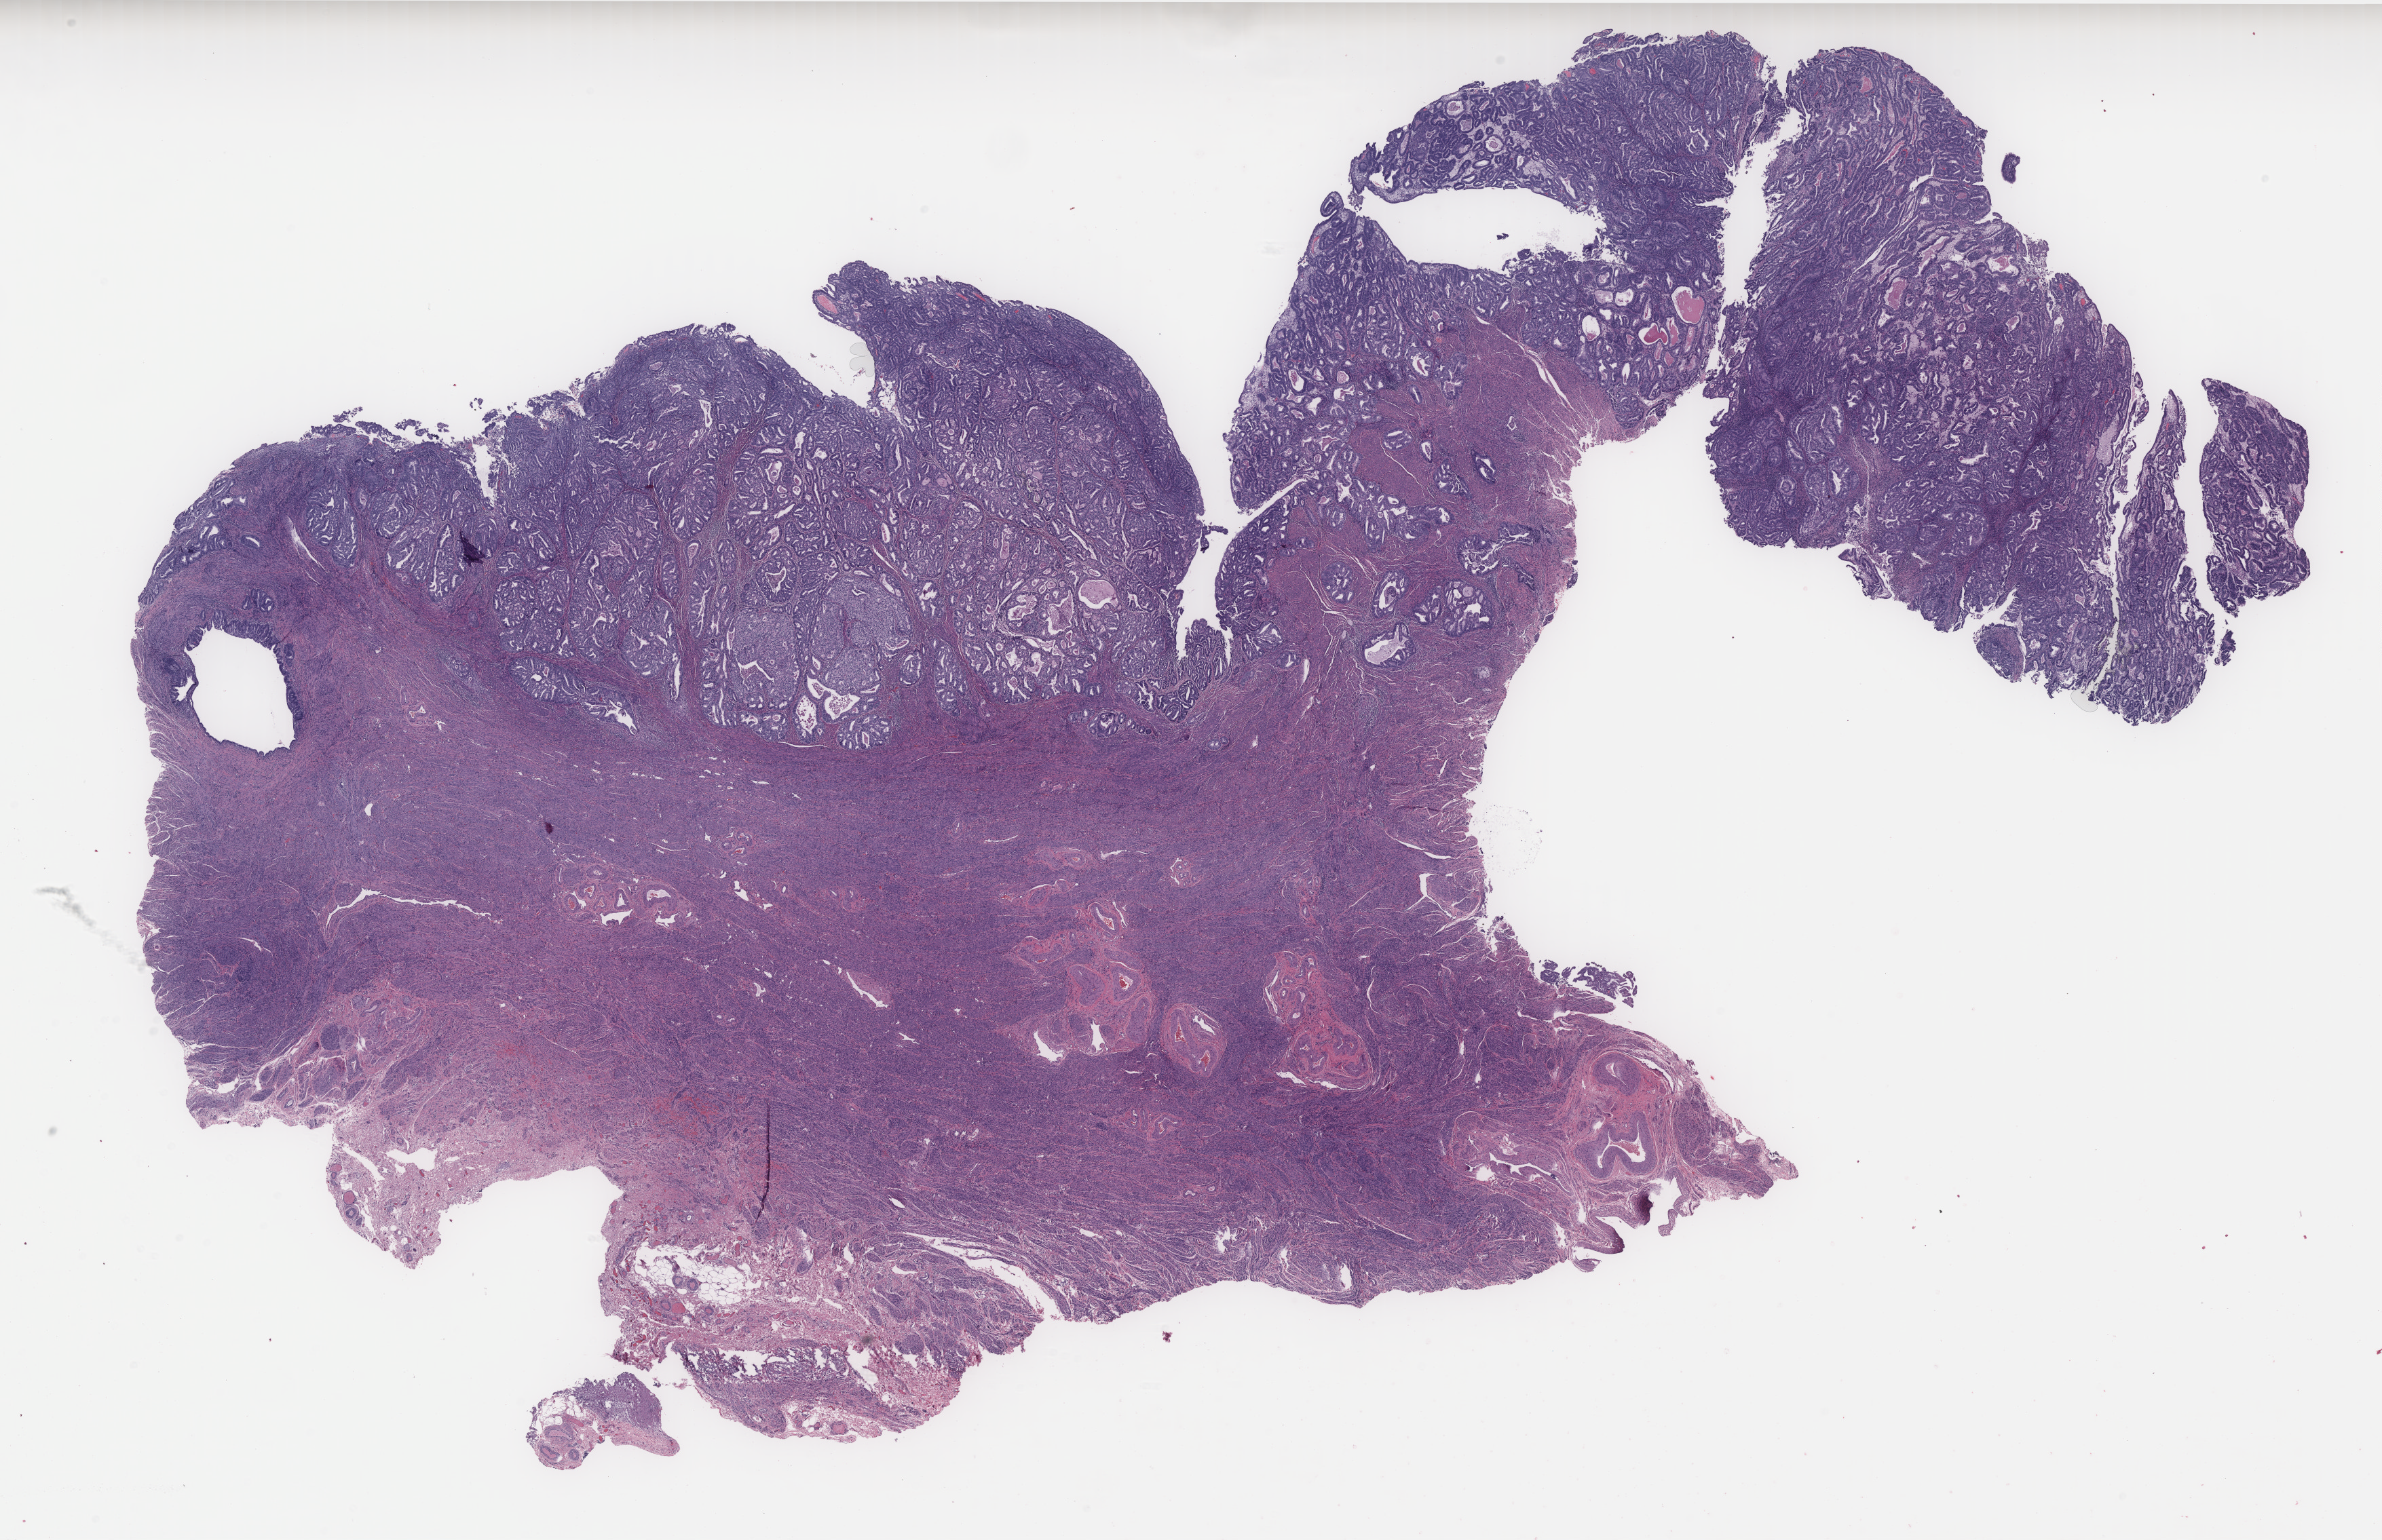
Whole-slide histology image, H&E-stained, shown as a low-resolution overview of the whole scanned area (about 28.1 x 18.2 mm, slide scanned at 40x). Formalin-fixed paraffin-embedded (FFPE) diagnostic section. Primary tumour sample from the uterus. Female patient; age at initial diagnosis 60 years. Histologic grade: G2 (moderately differentiated).
• FIGO stage: IIIC1
• pathologic diagnosis: Endometrioid adenocarcinoma, NOS (endometrium)